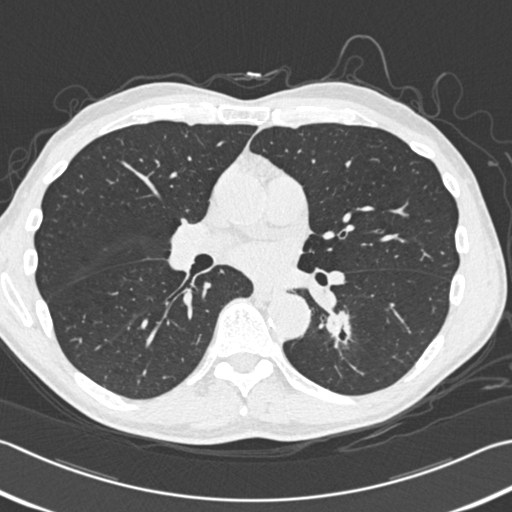
Low-dose screening chest CT, one axial slice. Lung window (W 1500 / L -600 HU). 1 mm slice thickness. 512 × 512 image matrix, field of view 346 × 346 mm.
Structures marked on this image (manually delineated by an expert):
- lesion 1 (tumor, lower lobe of left lung): bounding box <326,311,350,339> (left, top, right, bottom; pixels)